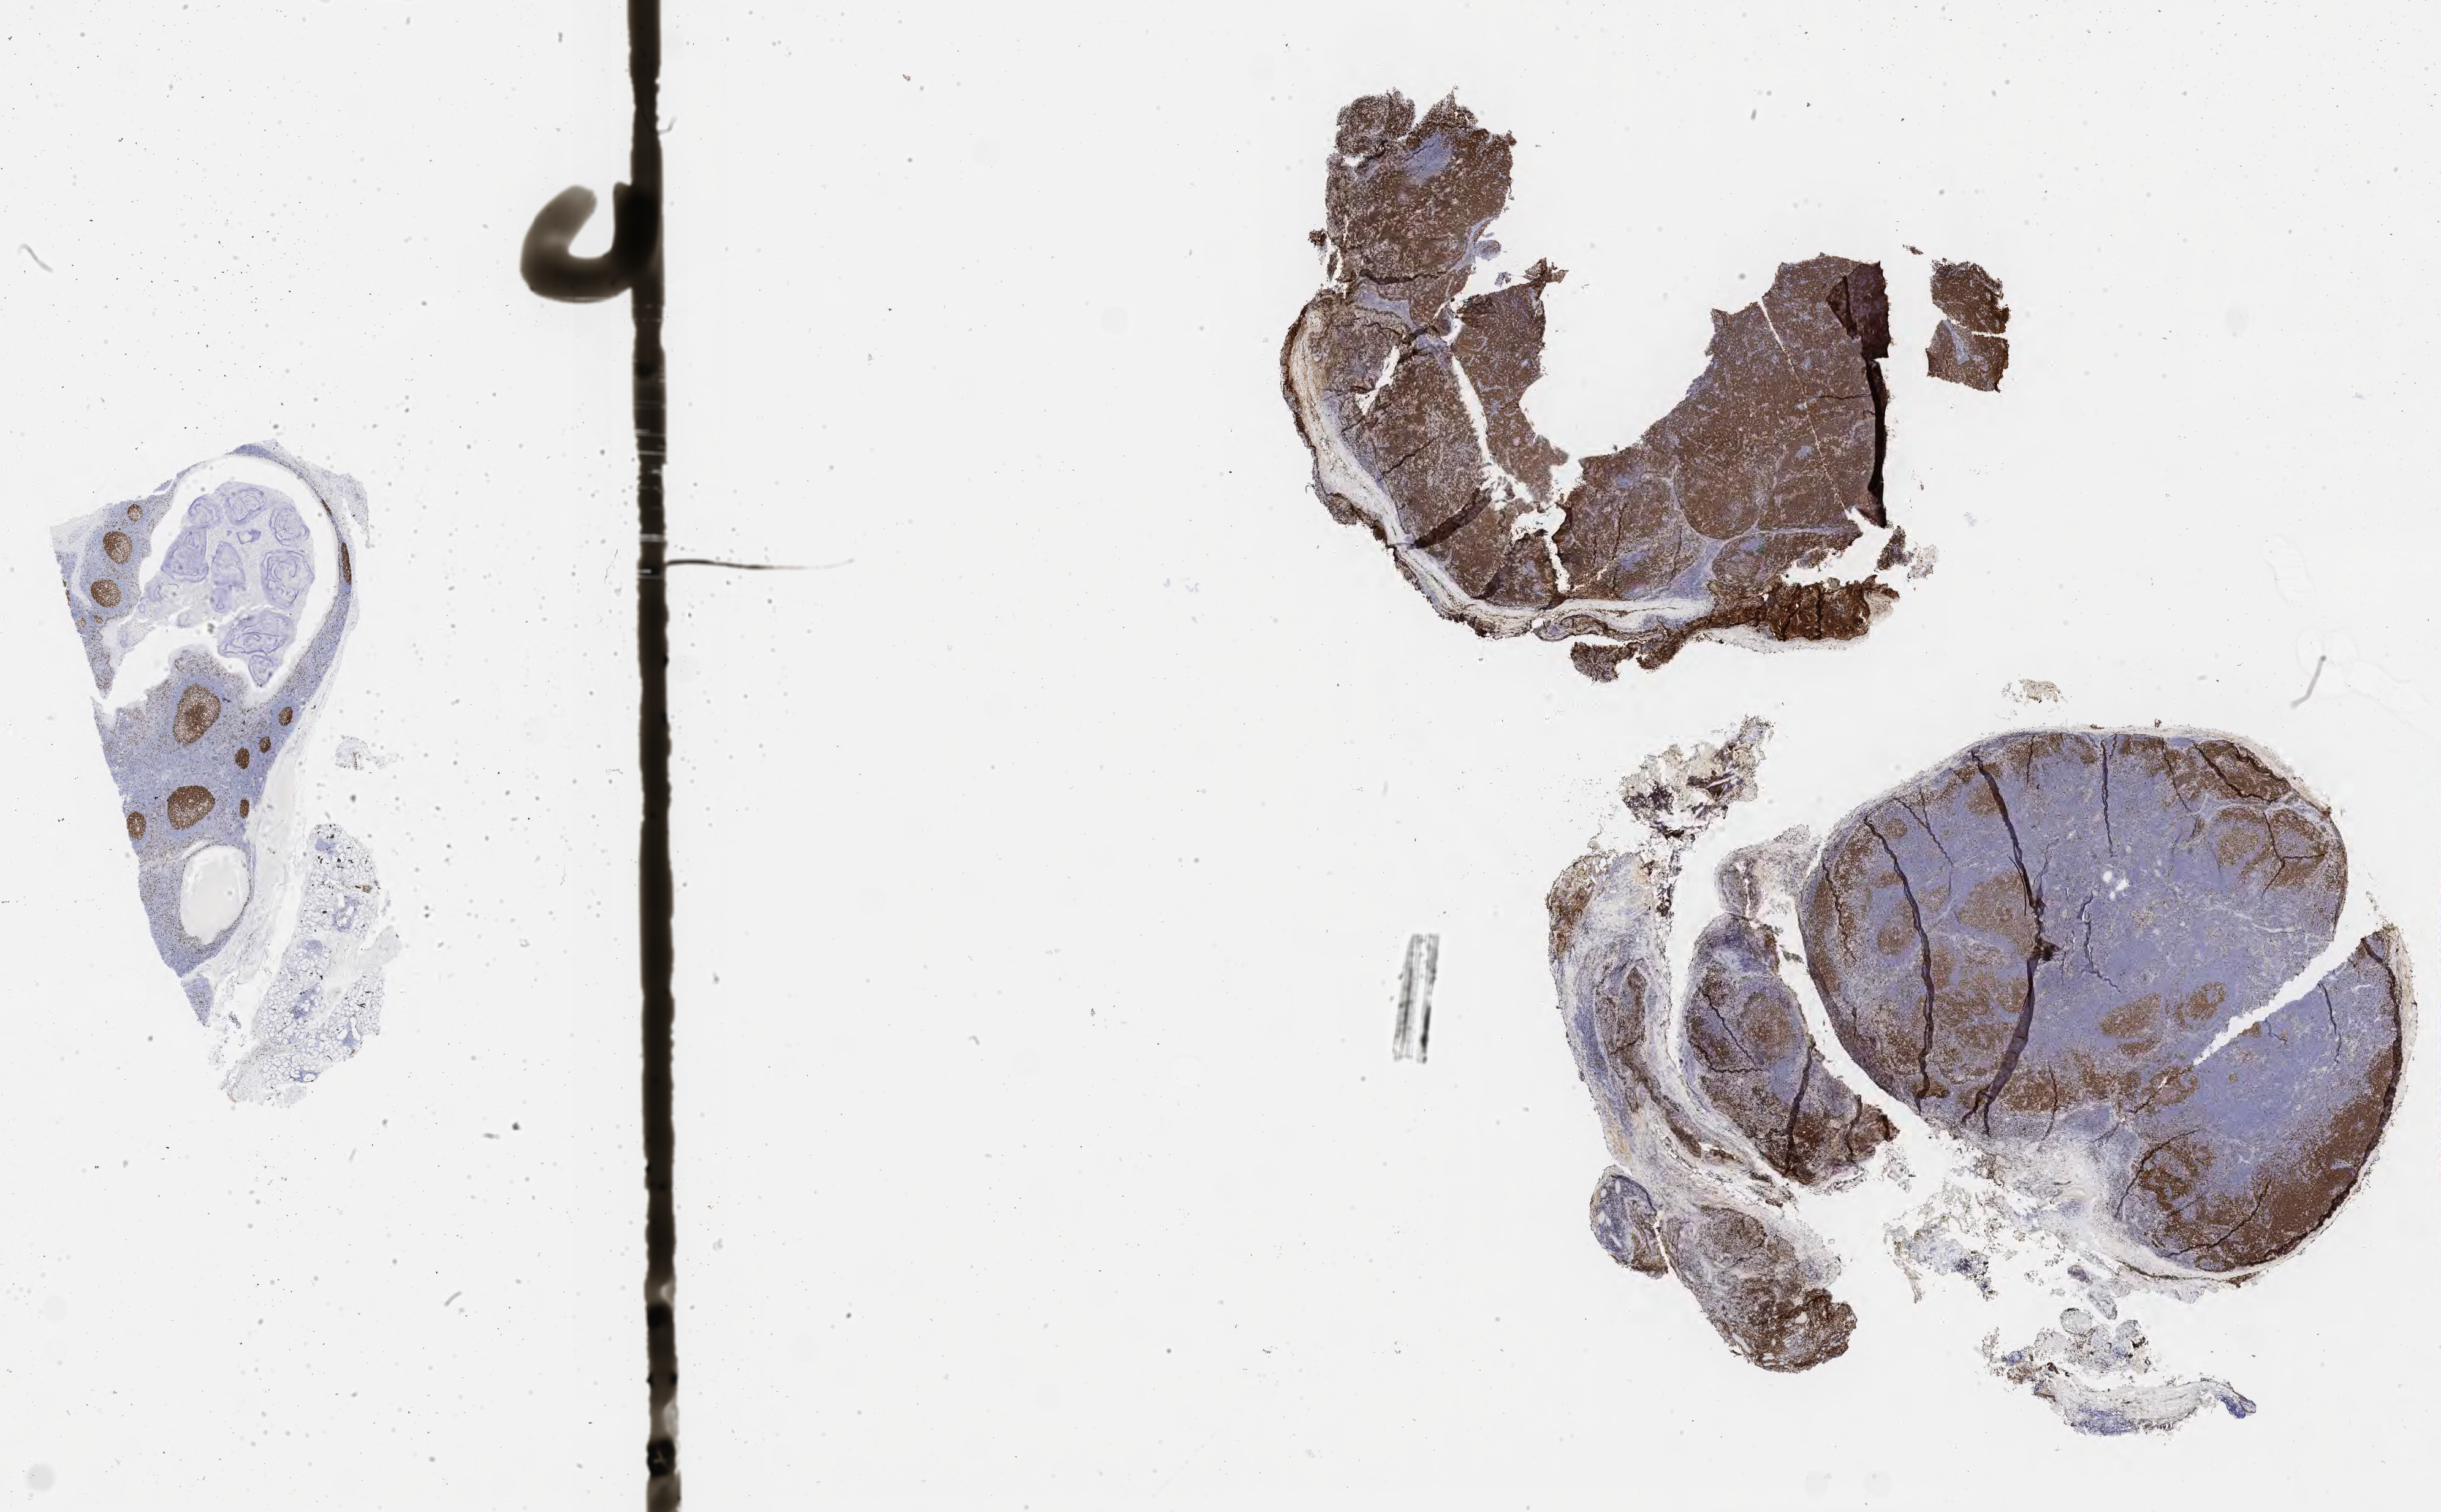
Whole-slide image, immunohistochemical stain for Ki-67 — shown as a low-resolution overview of the whole scanned area (about 32.2 x 19.9 mm), tumor tissue. Patient male; 25 years old.
Diagnosis: Burkitt lymphoma, NOS.